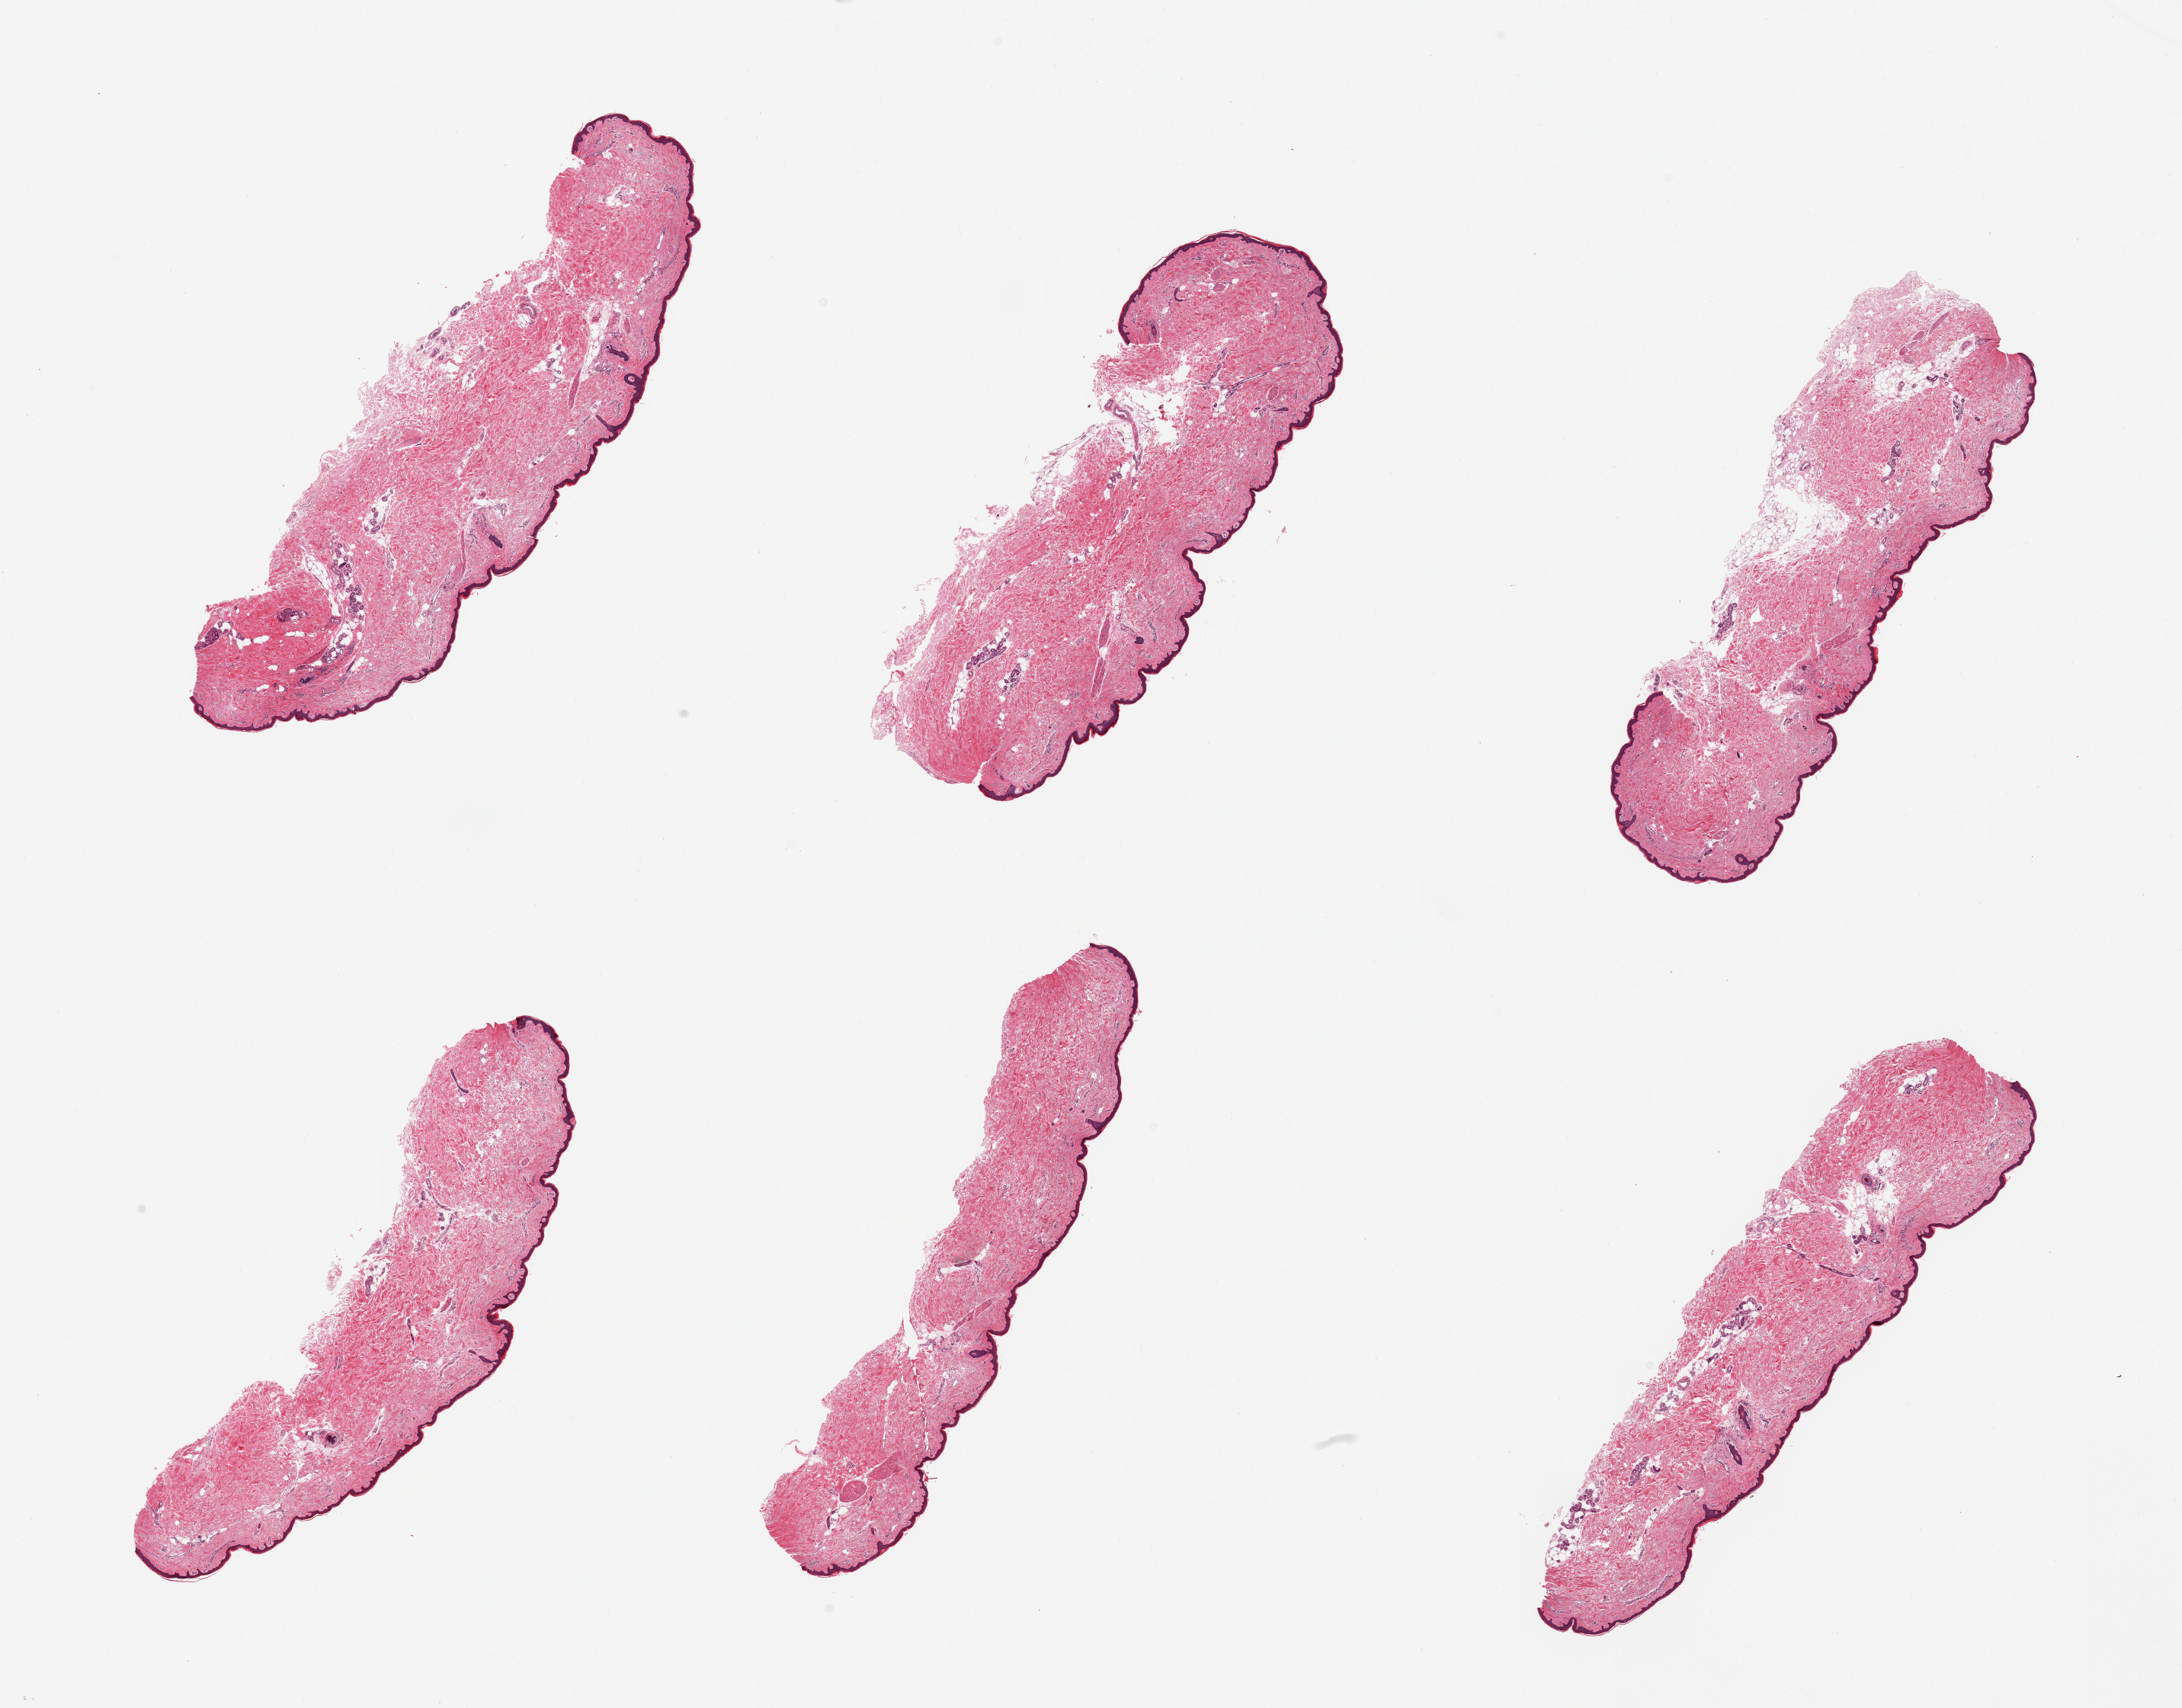
Whole-slide image, haematoxylin and eosin stain, shown as a low-resolution overview of the whole scanned area (about 22.6 x 17.7 mm); PAXgene-fixed paraffin-embedded (PFPE) section; sampled site (target tissue): skin of lower leg; donor tissue sample. Female donor.
Pathologist's review note for this sample: 6 pieces, trace adherent fat, squamous epithelium is ~30-40 microns.